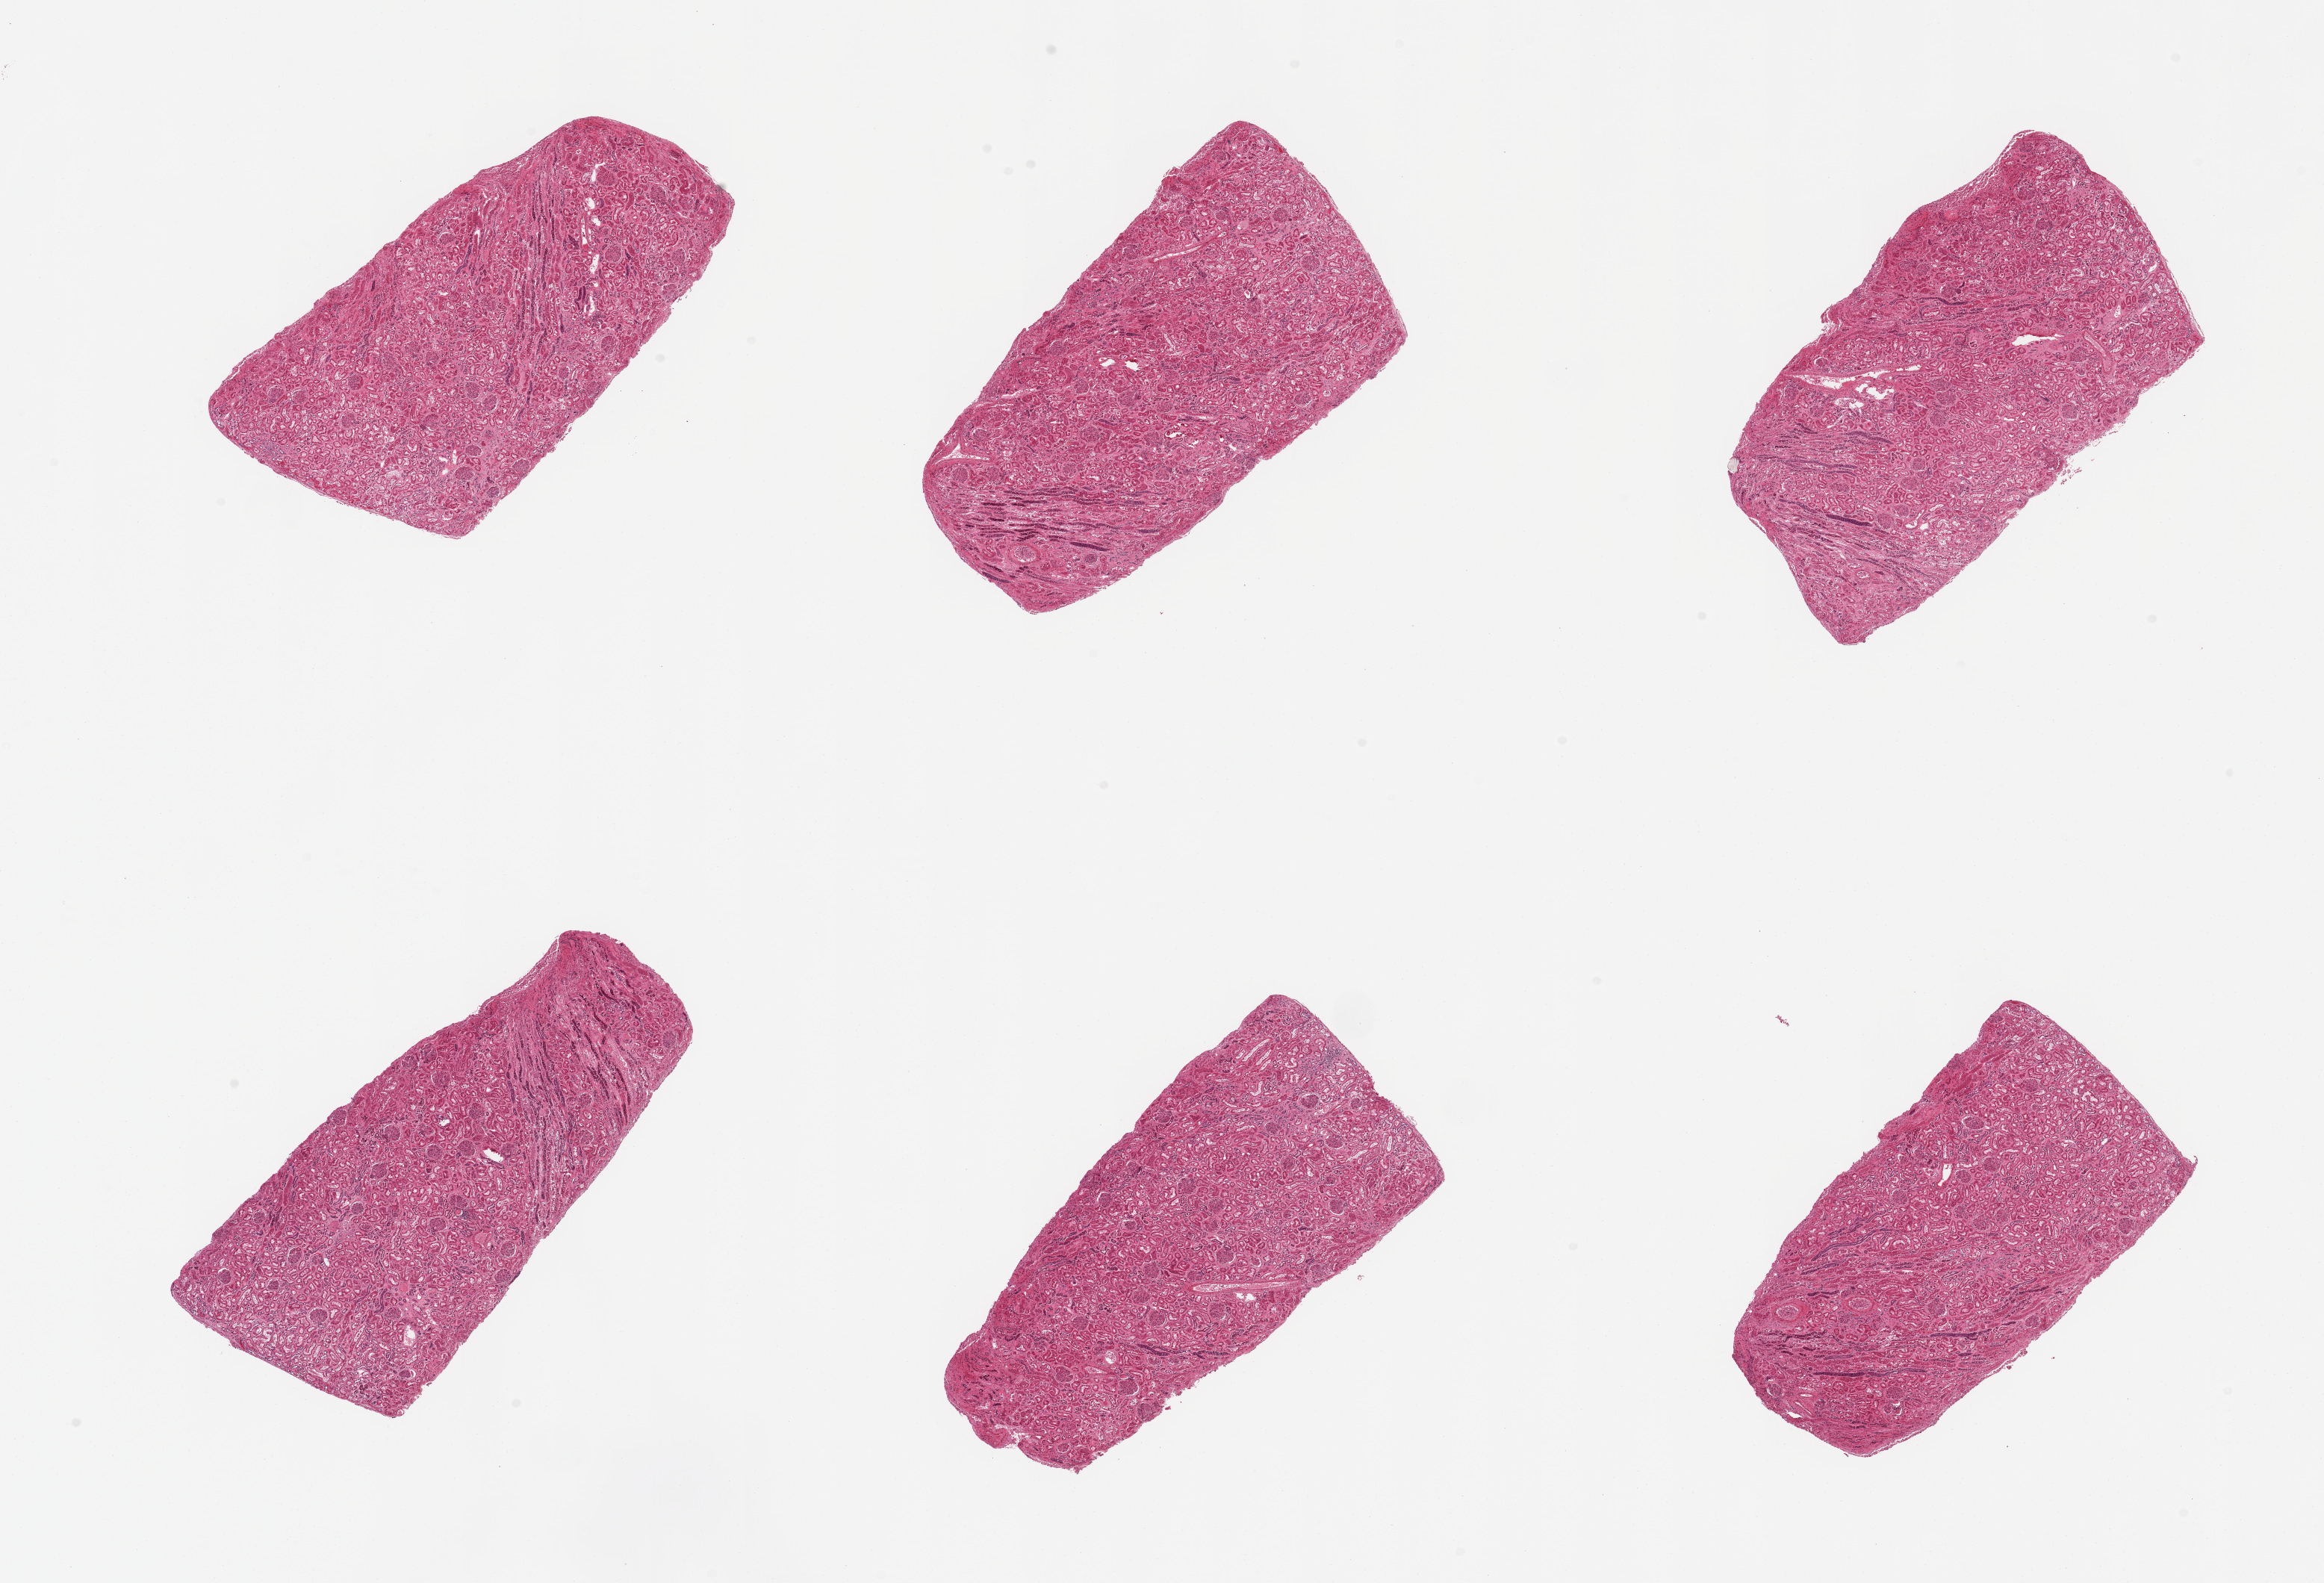
Digitized hematoxylin and eosin (H&E)-stained section, a low-resolution overview of the entire scanned area, about 24.6 x 16.8 mm (from a 20x scan). PAXgene-fixed, paraffin-embedded tissue. Target tissue: renal cortex. Tissue donor sample. Donor: female.
• review note (as recorded): 6 pieces; glomeruli in all sections